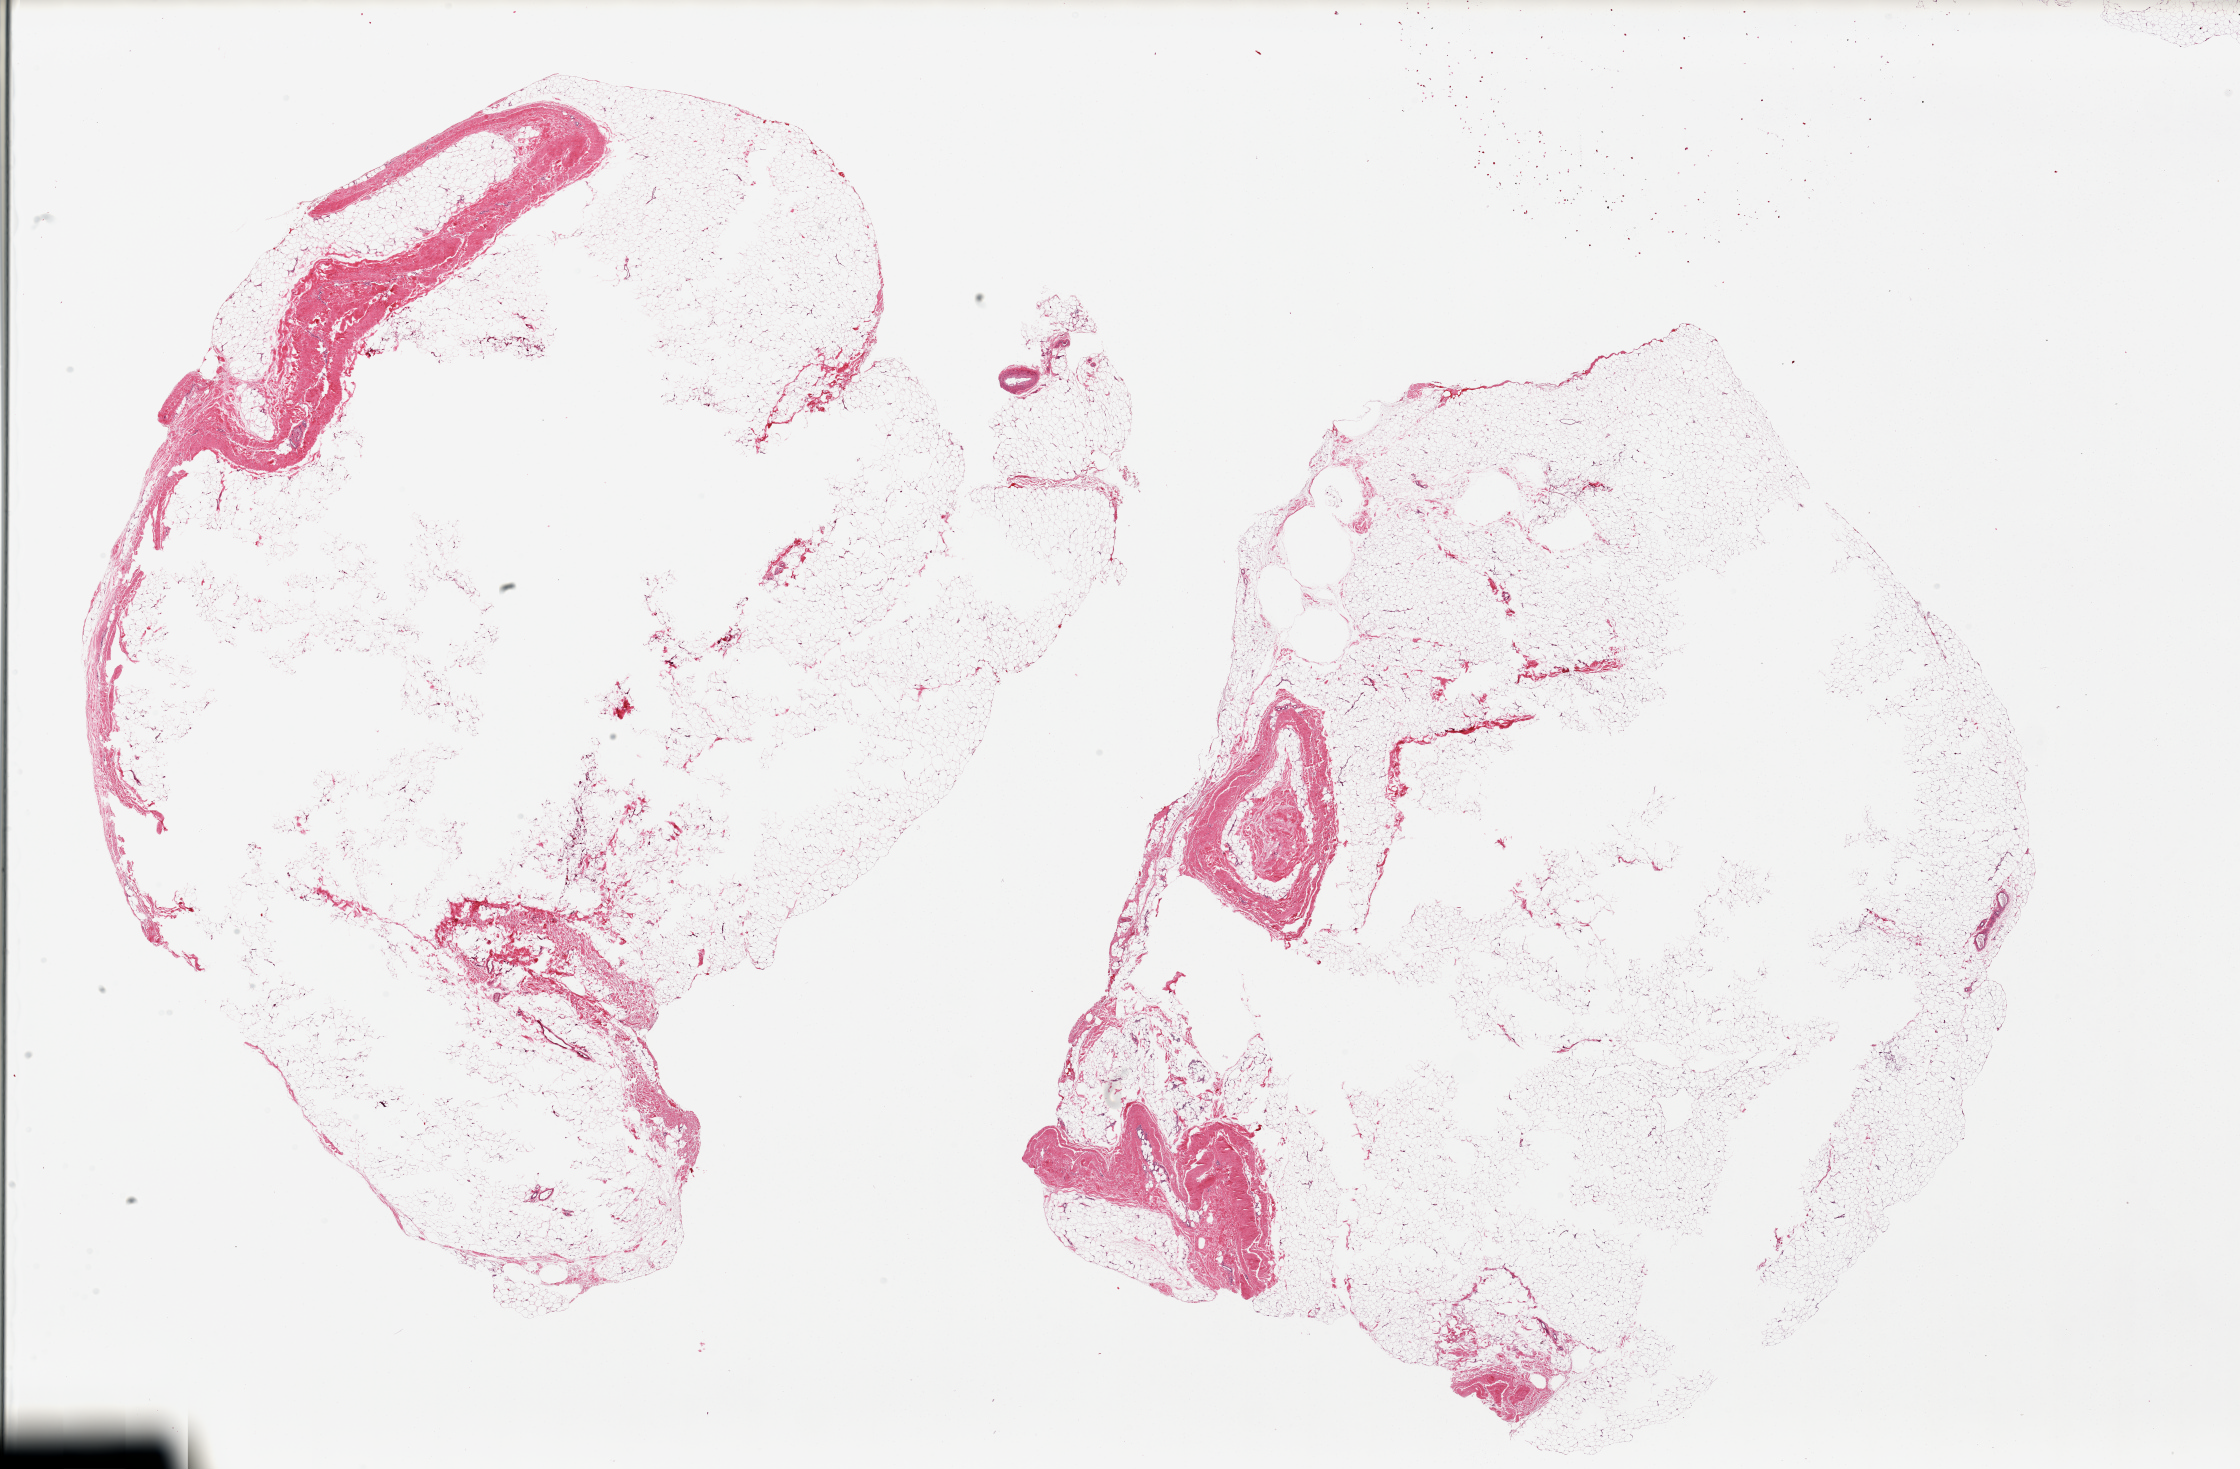
Haematoxylin and eosin whole-slide image, brightfield, shown as a low-resolution overview of the whole scanned area (about 35.4 x 23.2 mm); PAXgene-fixed paraffin-embedded (PFPE) section; target tissue: adipose tissue; donor tissue sample. Male donor.
Review note (as recorded): 2 pieces; central holes in both; 5-10% fibrous tissue.